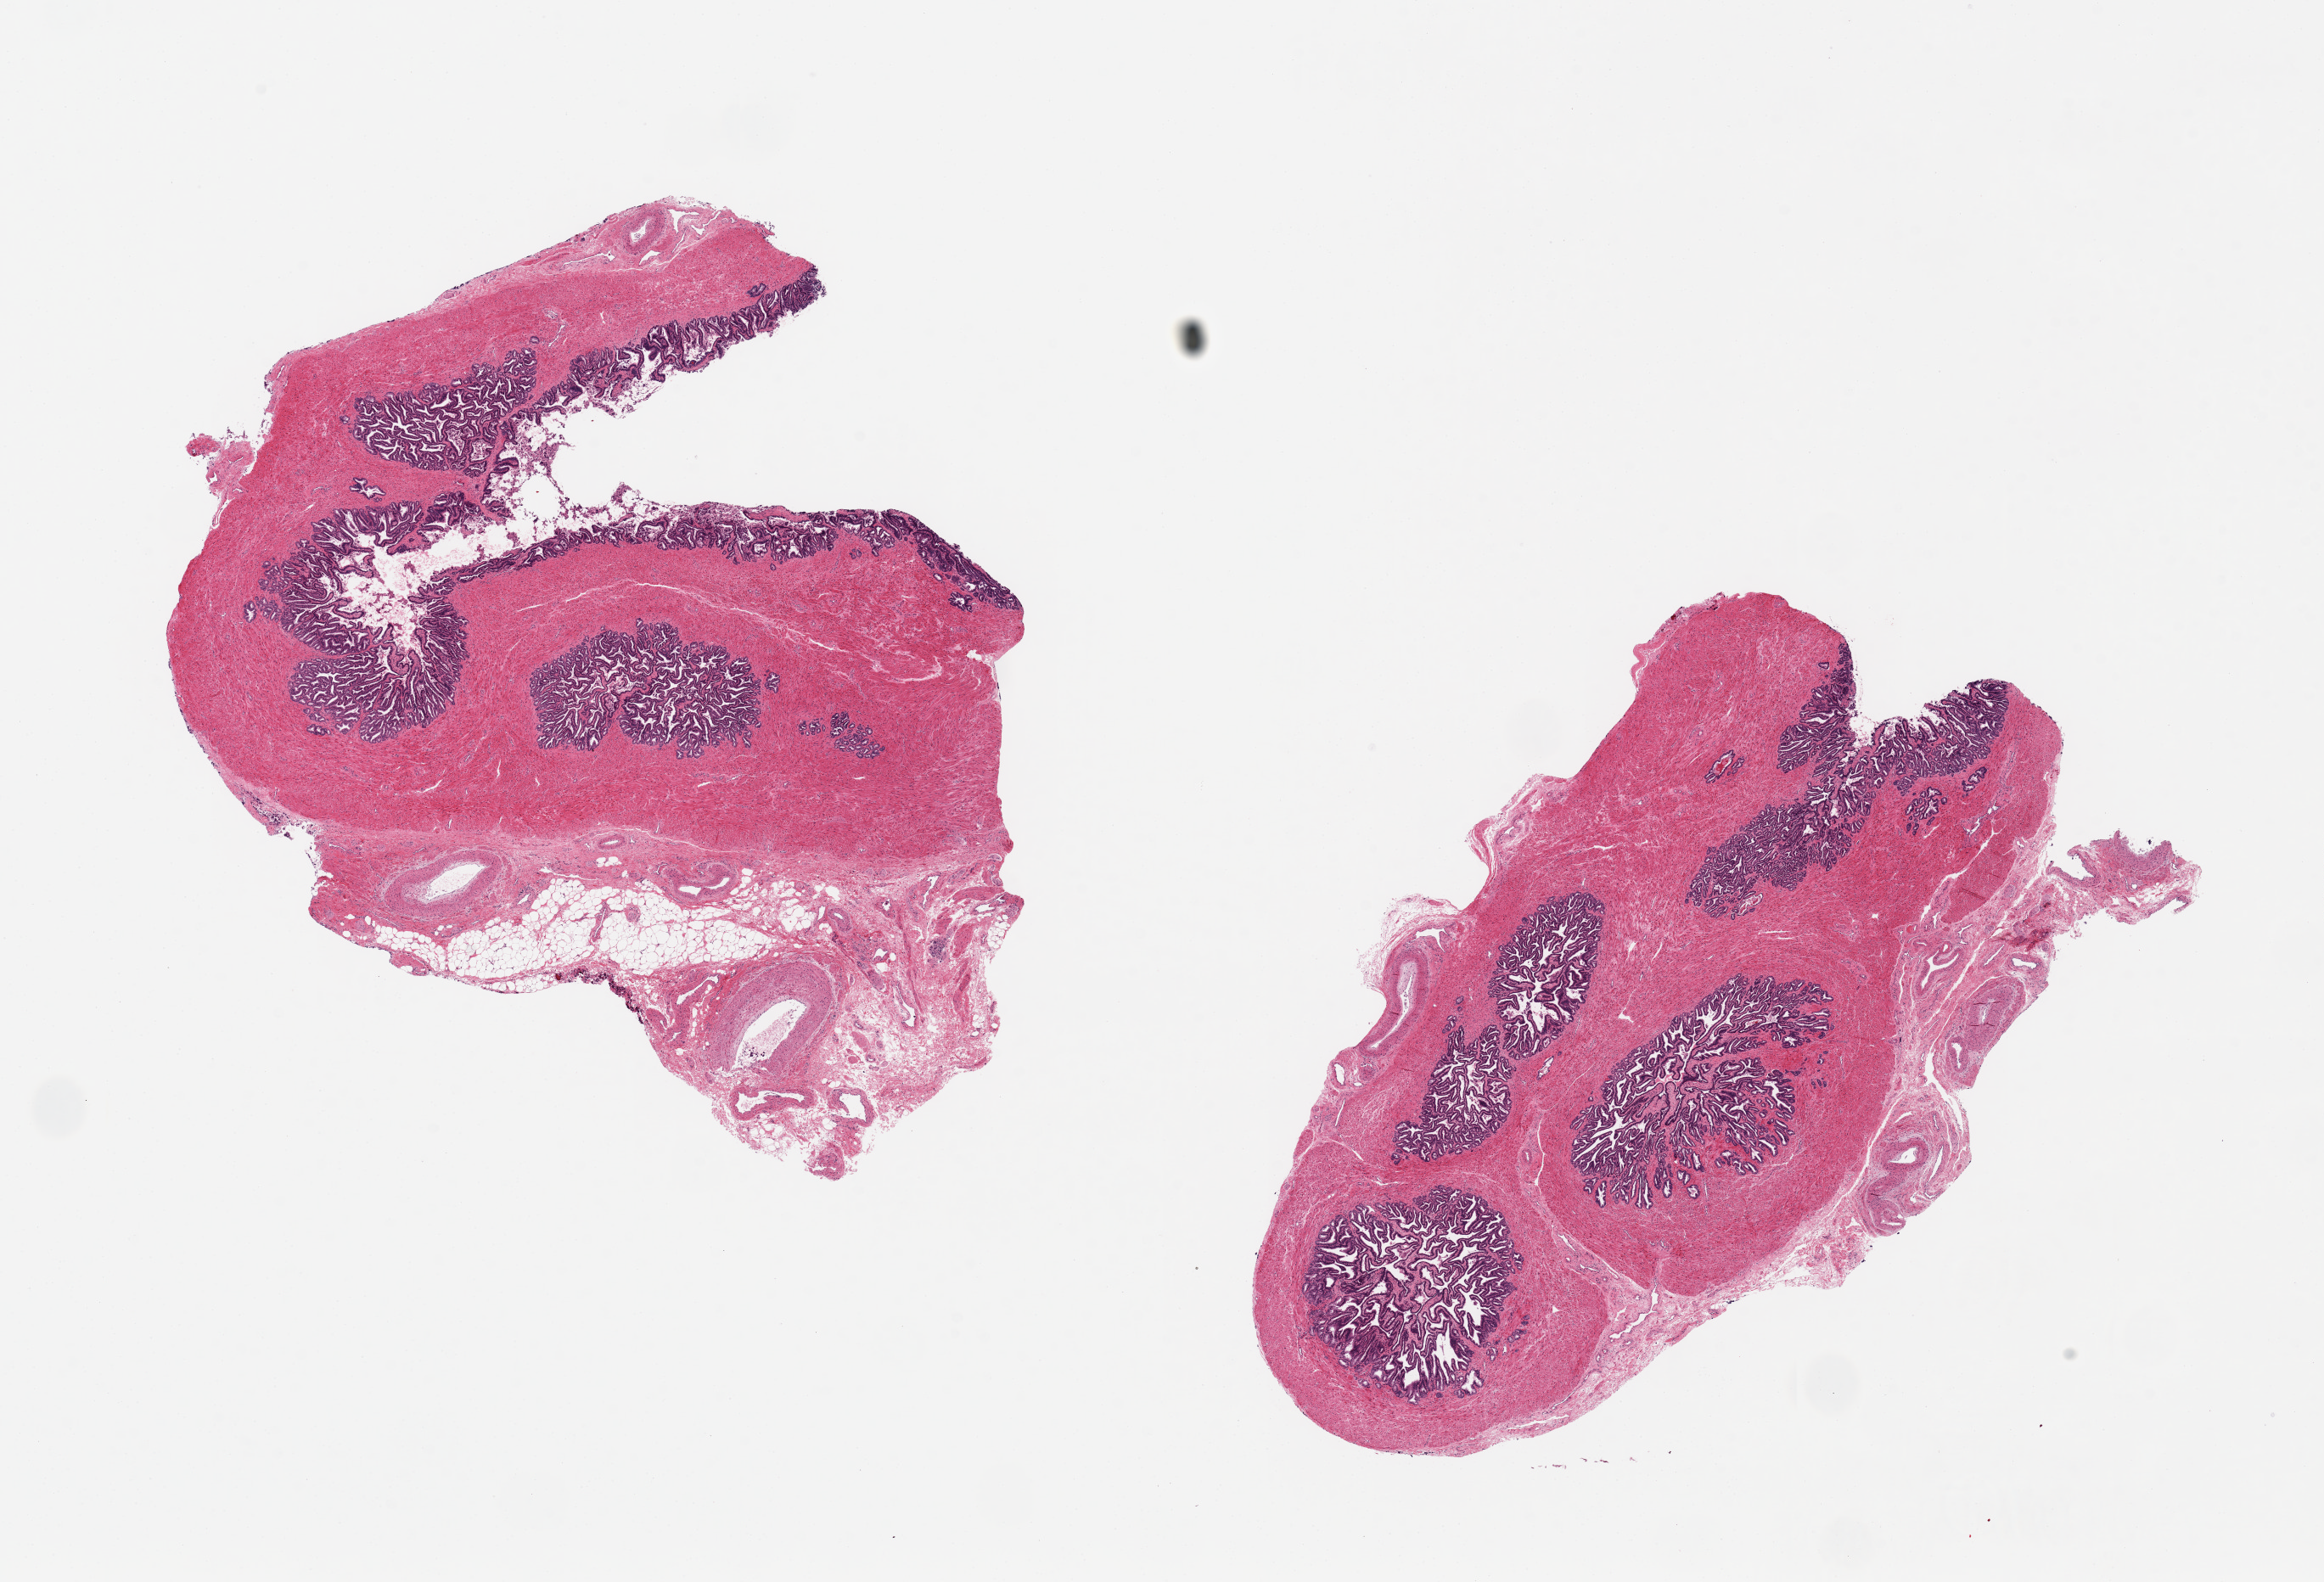
H&E whole-slide image, low-resolution overview of the scanned area, about 21.7 x 14.7 mm (acquisition: 20x scan). PAXgene-fixed, paraffin-embedded tissue. Sampled site (target tissue): prostate. Tissue donor sample. Male donor.
• review note (as recorded): 2 pieces, not prostate but seminal vesicle